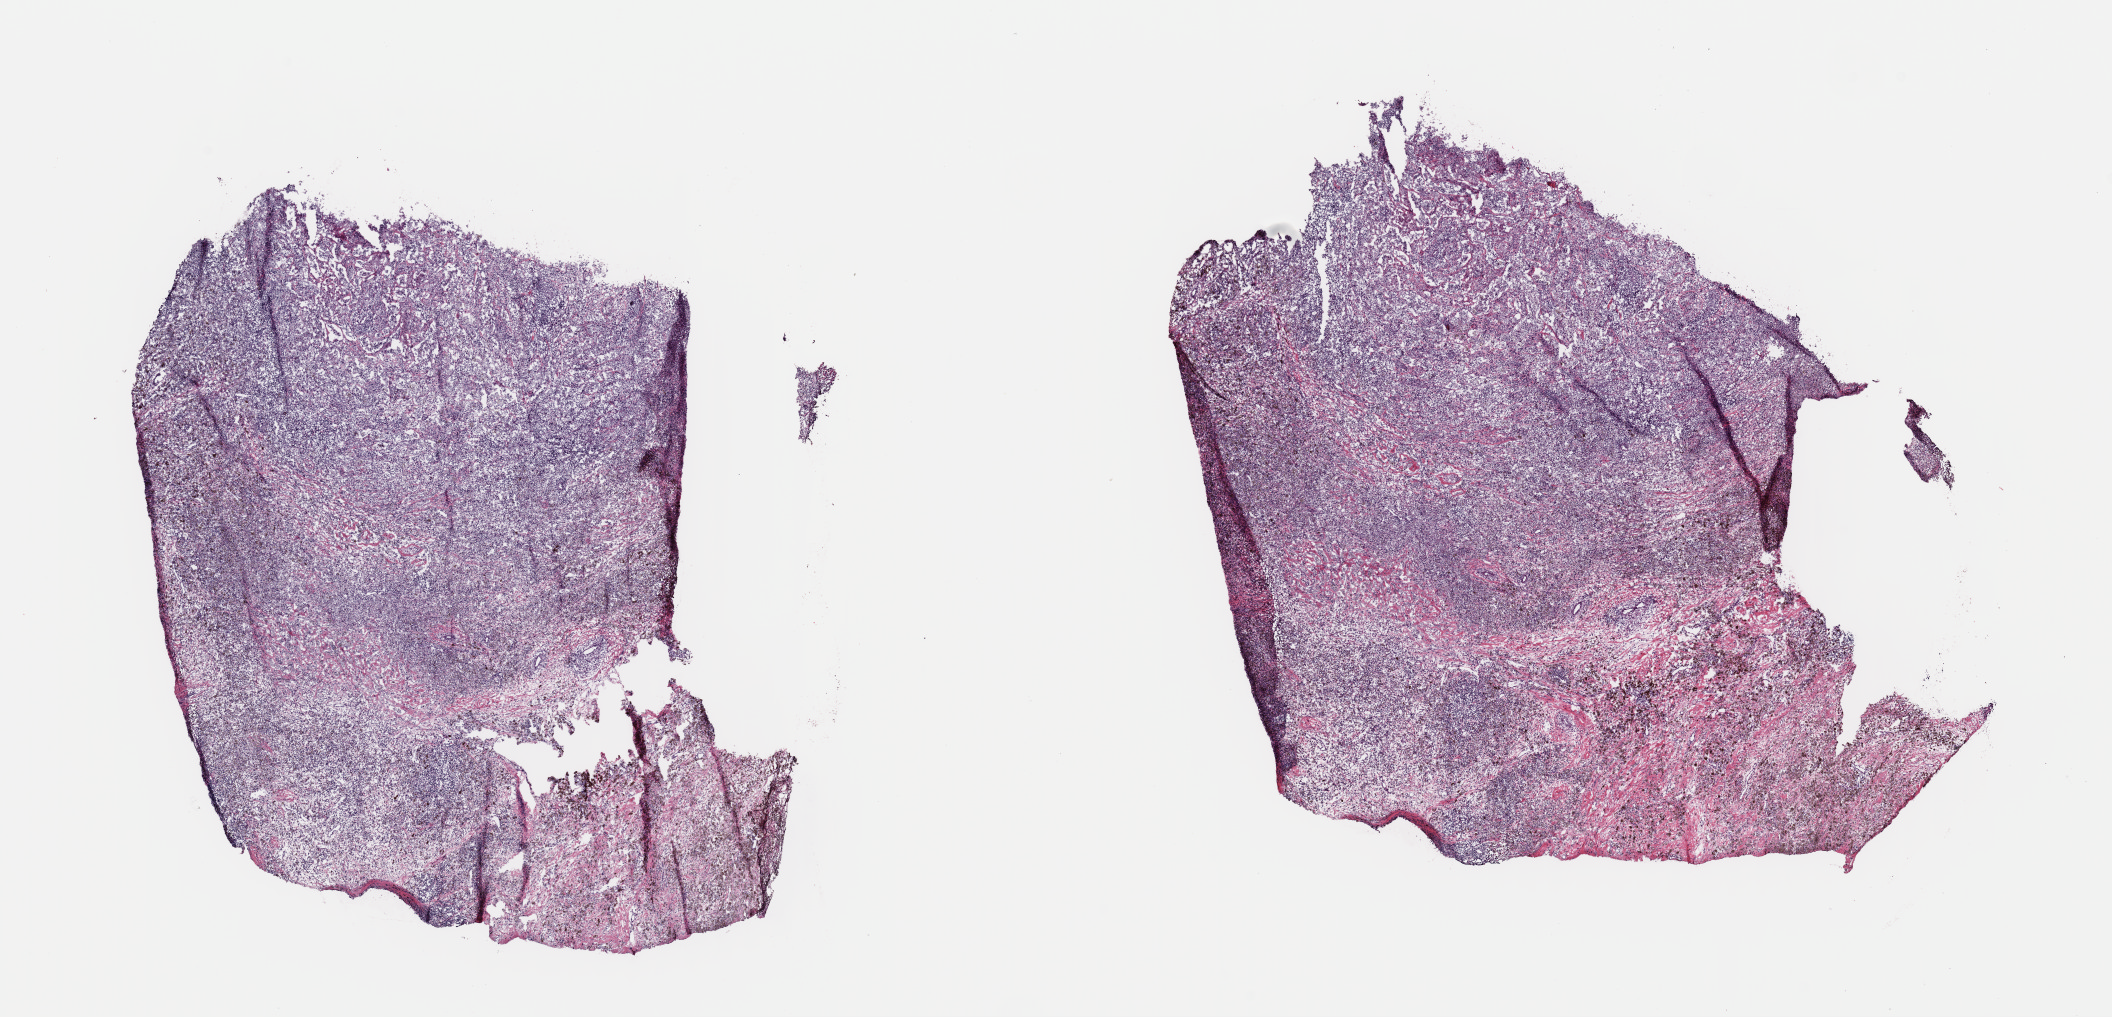
Digitized Hematoxylin and eosin (H&E) stained tissue section (whole slide), whole scanned area (about 16.7 x 8.0 mm, from a 40x scan) shown as a low-resolution overview, frozen section from the top of the tissue portion, metastatic tumour sample. Male, age 55 years at initial diagnosis. Composition of this section per pathologist review: tumour cells 70%, tumour nuclei 70%.
This section: metastatic tumour tissue. Patient diagnosis: Malignant melanoma, NOS.